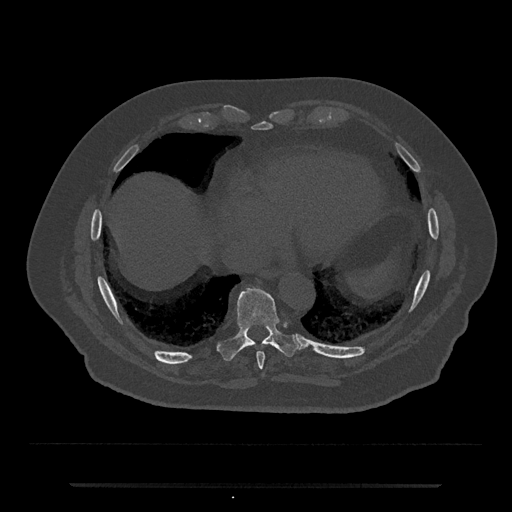
CT including the spine, one axial slice; position 769 of 797 along the scan axis; reconstruction kernel Br40s/3; 120 kVp; bone window (W 1800 / L 400 HU); 512 × 512 image matrix, field of view 434 × 434 mm. Male patient, age 80 years. Case-level facts recorded for this patient, not image findings: primary cancer: prostate; vertebrae with lytic lesions (as recorded): L1, T11.
Outlined on this slice (semi-automatically segmented with operator editing):
- T8 vertebra: box from (x=256, y=352) to (x=265, y=370) px
- T9 vertebra: (x=218, y=286)–(x=302, y=361)